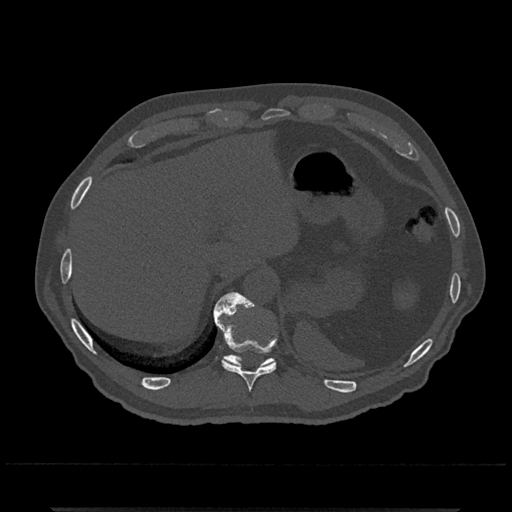
CT including the spine, one axial slice. Position 535 of 797 along the scan axis. Reconstruction kernel Br40s/3. 120 kVp. Bone window (W 1800 / L 400 HU). 0.5 mm slice thickness. 512 × 512 image matrix, field of view 393 × 393 mm. Patient: male, 67 years. From the clinical record (not read from this slice): primary cancer: prostate.
Outlined on this slice (semi-automatically segmented with operator editing):
- T10 vertebra: bounding box <214,292,276,392> (left, top, right, bottom; pixels)
- T11 vertebra: <213,293,276,367>